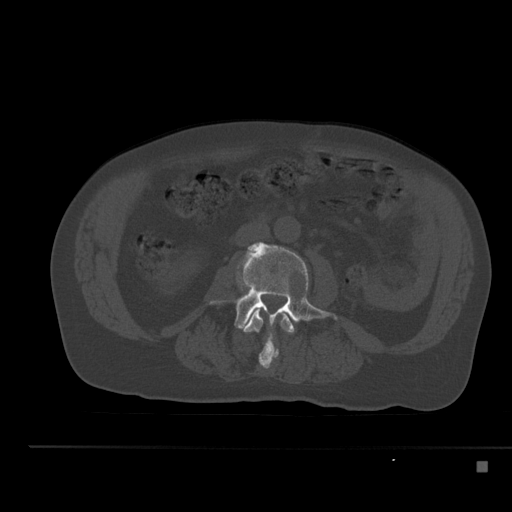
CT including the spine, one axial slice; position 169 of 517 along the scan axis; reconstruction kernel Br40s; 120 kVp; bone window (W 1800 / L 400 HU); 1.5 mm slice thickness; 512 × 512 image matrix, field of view 408 × 408 mm. Patient: male, 70 years. Case-level facts recorded for this patient, not image findings: primary cancer: renal; vertebrae with lytic lesions (as recorded): T4, T6, T10, T12, L3, L4, L5.
Structures marked on this image (semi-automatically segmented with operator editing):
- L2 vertebra: bounding box (x1, y1, x2, y2) in pixels: (241, 310, 295, 370)
- L3 vertebra: (234, 240, 338, 329)